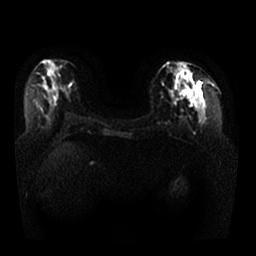
Breast MRI, one axial slice; position 13 of 25 along the scan axis; diffusion-weighted series; image 2 of 4 stored at this slice position (different b-values; order by instance number); 1.5 T; 4 mm slice thickness; 256 × 256 image matrix. Female patient.
Structures marked on this image (manually delineated by an expert):
- tumour on diffusion-weighted imaging: box from (x=182, y=86) to (x=192, y=98) px